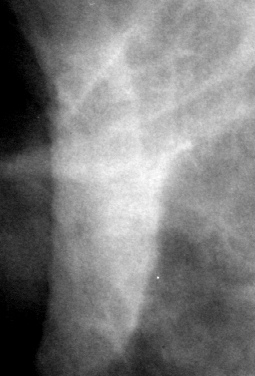
Region of interest cut from a scanned film mammogram (one marked finding), right breast, MLO view.
- Marked abnormality: mass, shape architectural distortion; BI-RADS assessment category 2; pathology (as recorded): benign.